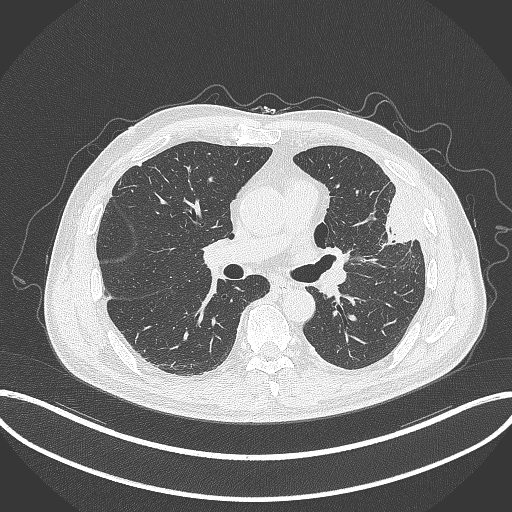
Chest CT, one axial slice. Position 185 of 382 along the scan axis. Reconstruction kernel B70f. Lung window (W 1500 / L -600 HU). 1 mm slice thickness. 512 × 512 image matrix, field of view 415 × 415 mm. Patient: male, 64 years. From the clinical record (not read from this slice): clinical TNM (as recorded): T4 N1 M0.
Outlined on this slice (rectangle marked by the reading radiologist):
- lung tumour (recorded histology: adenocarcinoma): box from (x=371, y=190) to (x=419, y=252) px